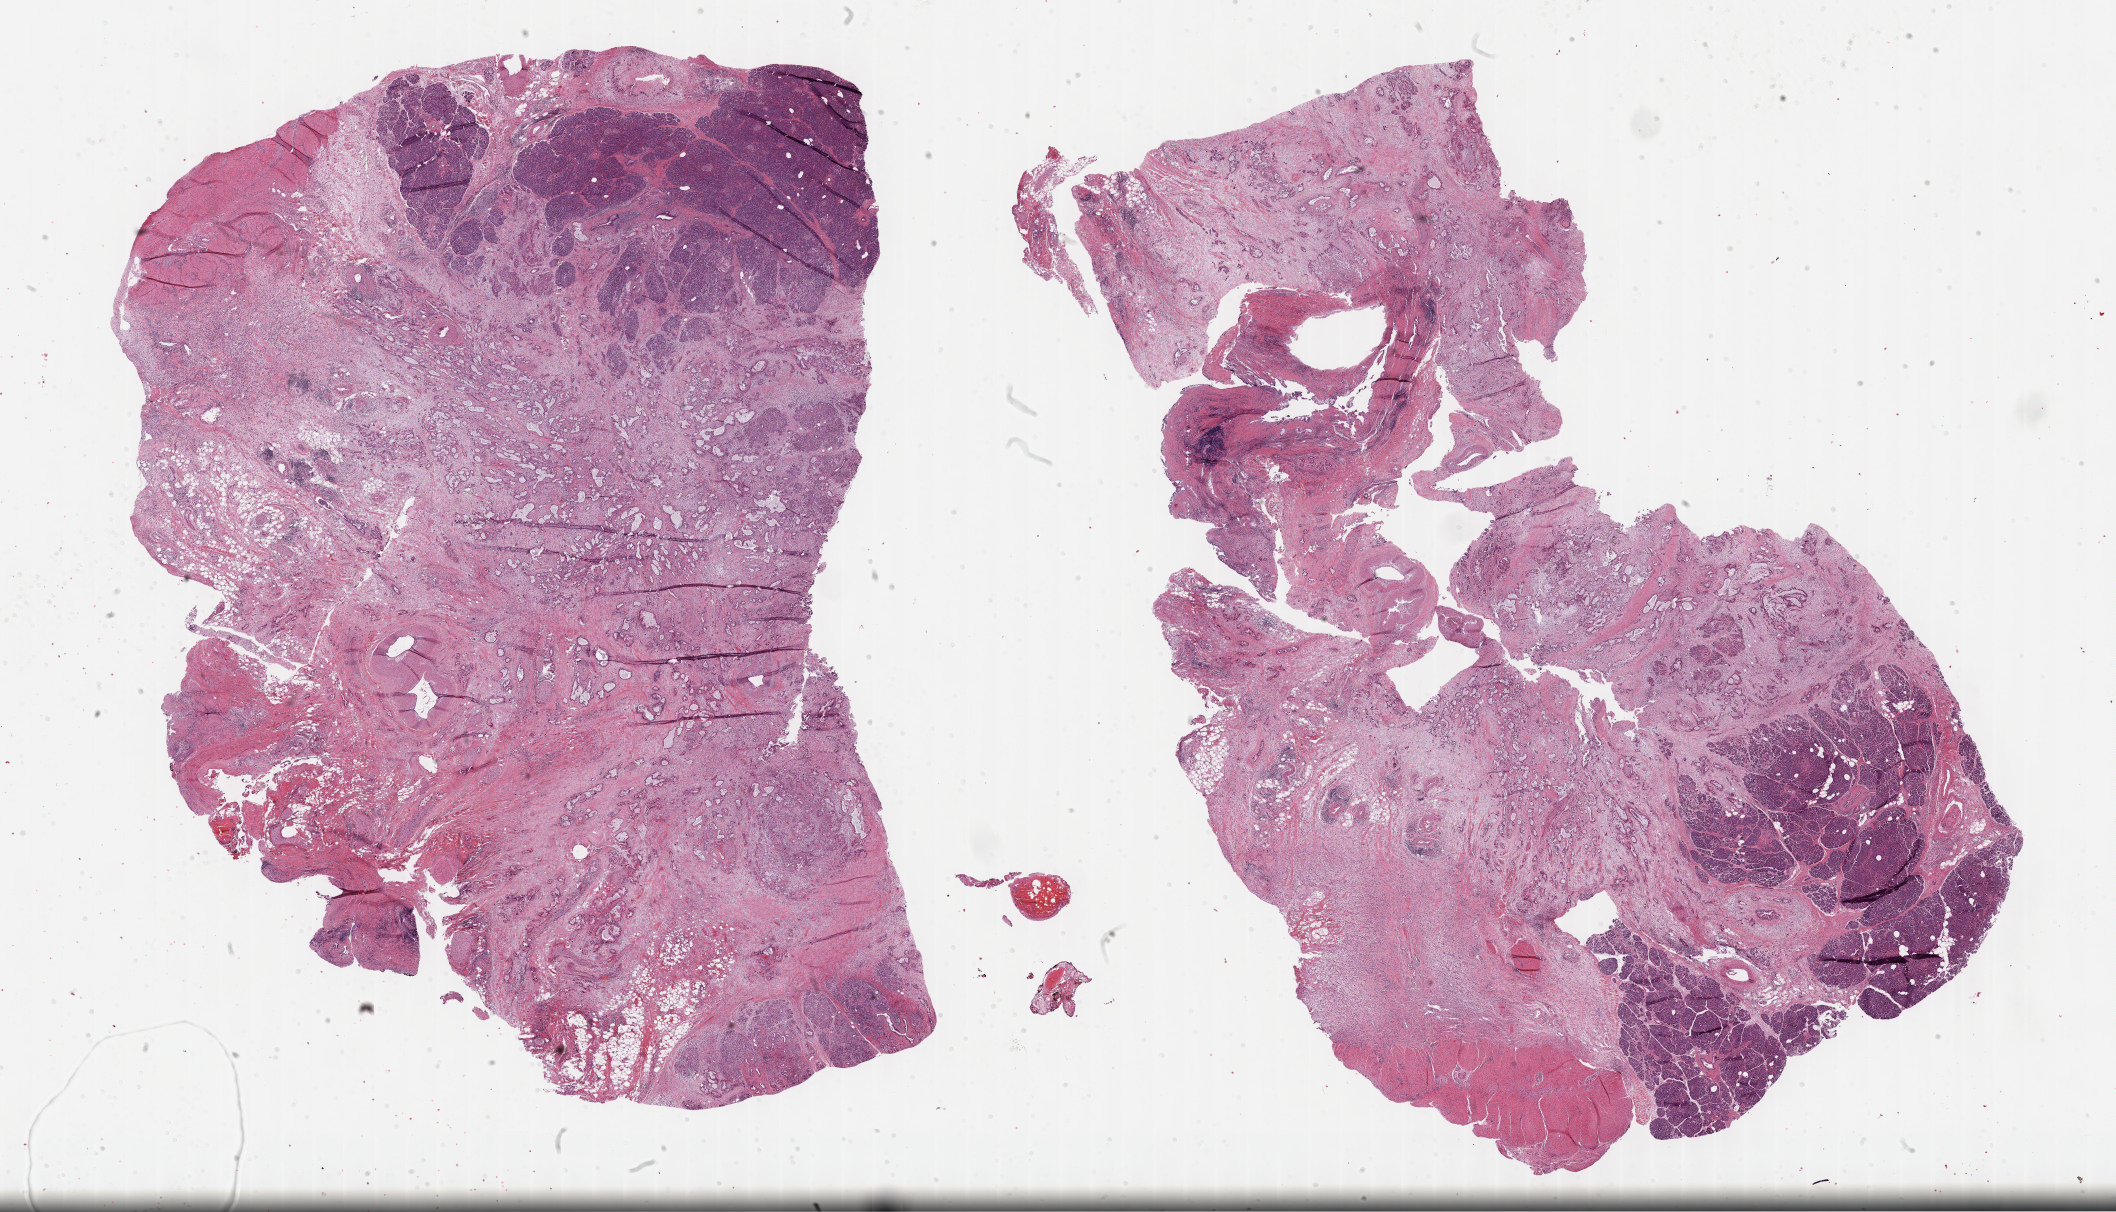
Whole-slide histology image, H&E-stained, shown as a low-resolution overview of the whole scanned area (about 34.2 x 19.6 mm); formalin-fixed paraffin-embedded (FFPE) diagnostic section; sample: primary tumour, pancreas. Patient: female, age at initial diagnosis 60 years. Histologic grade: G3 (poorly differentiated).
Diagnosis: Infiltrating duct carcinoma, NOS (overlapping lesion of pancreas). AJCC pathologic stage: IIA (7th edition).